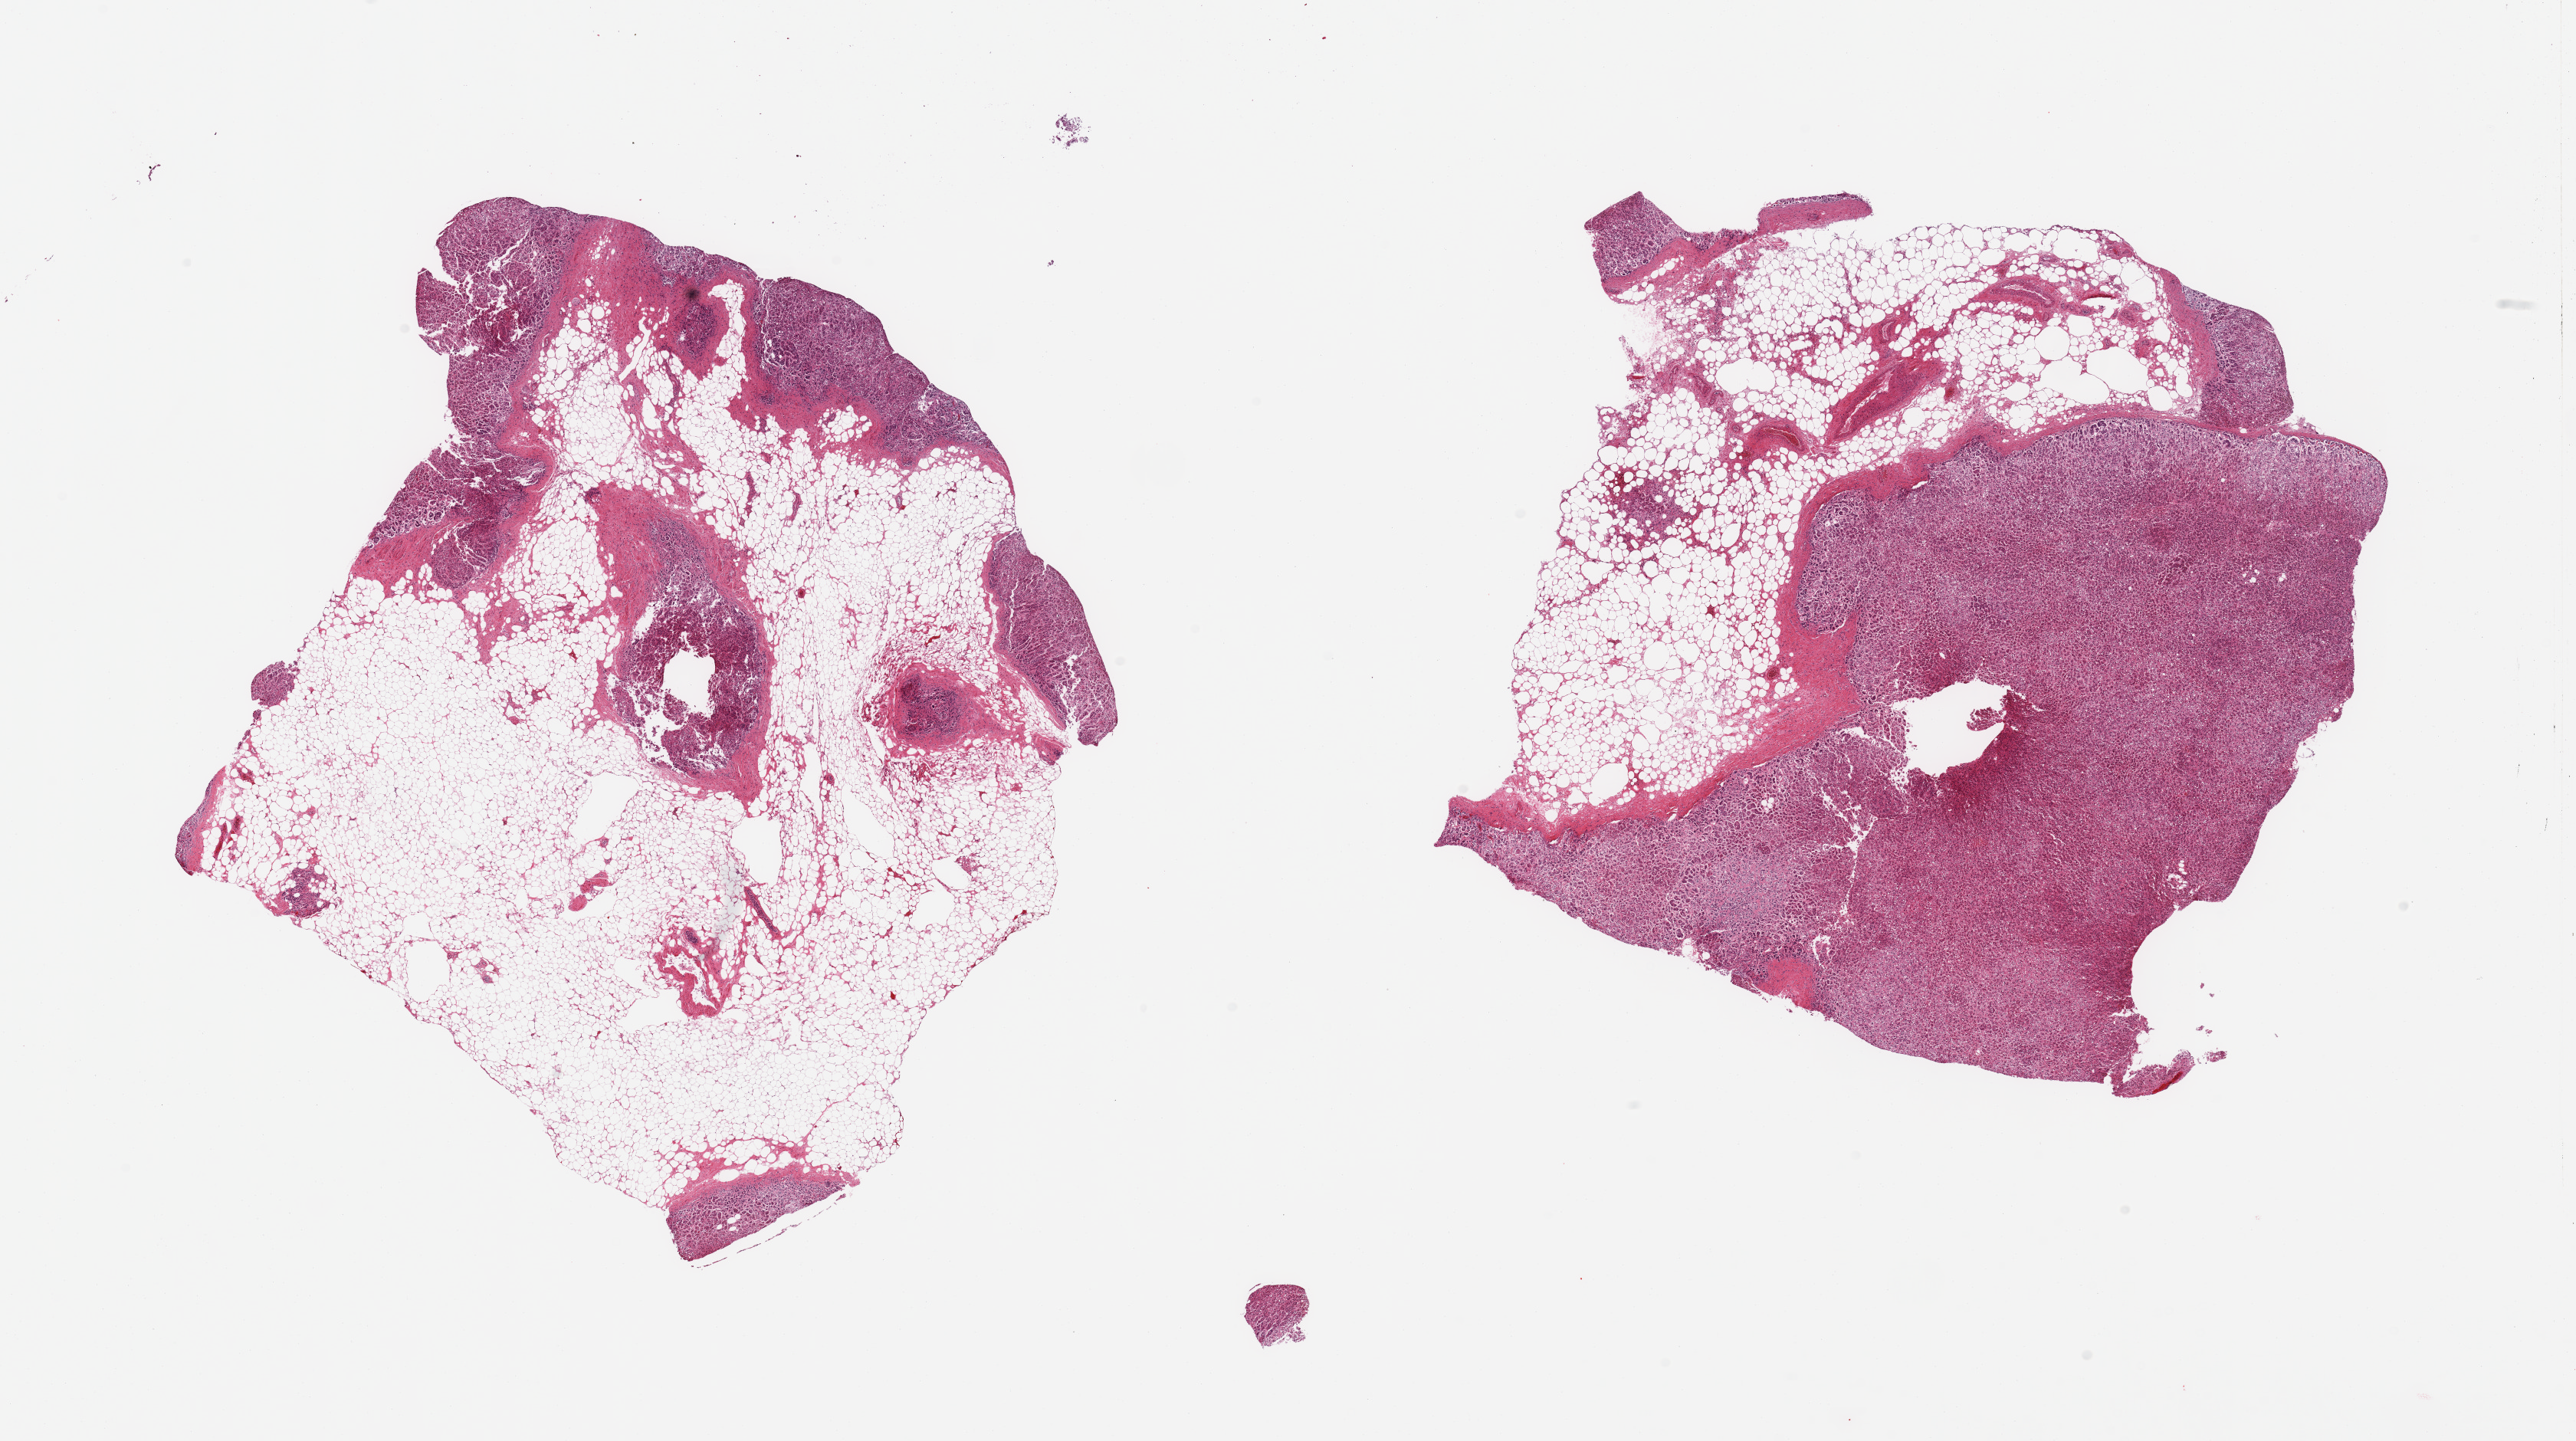
Digitized H&E-stained section — low-resolution overview of the scanned area, about 26.6 x 14.9 mm. PAXgene-fixed paraffin-embedded (PFPE) section. Sampled site (target tissue): adrenal gland. Donor tissue sample.
- pathologist's review note for this sample: 2 pieces; moderately autolyzed, 75% and 40% fat